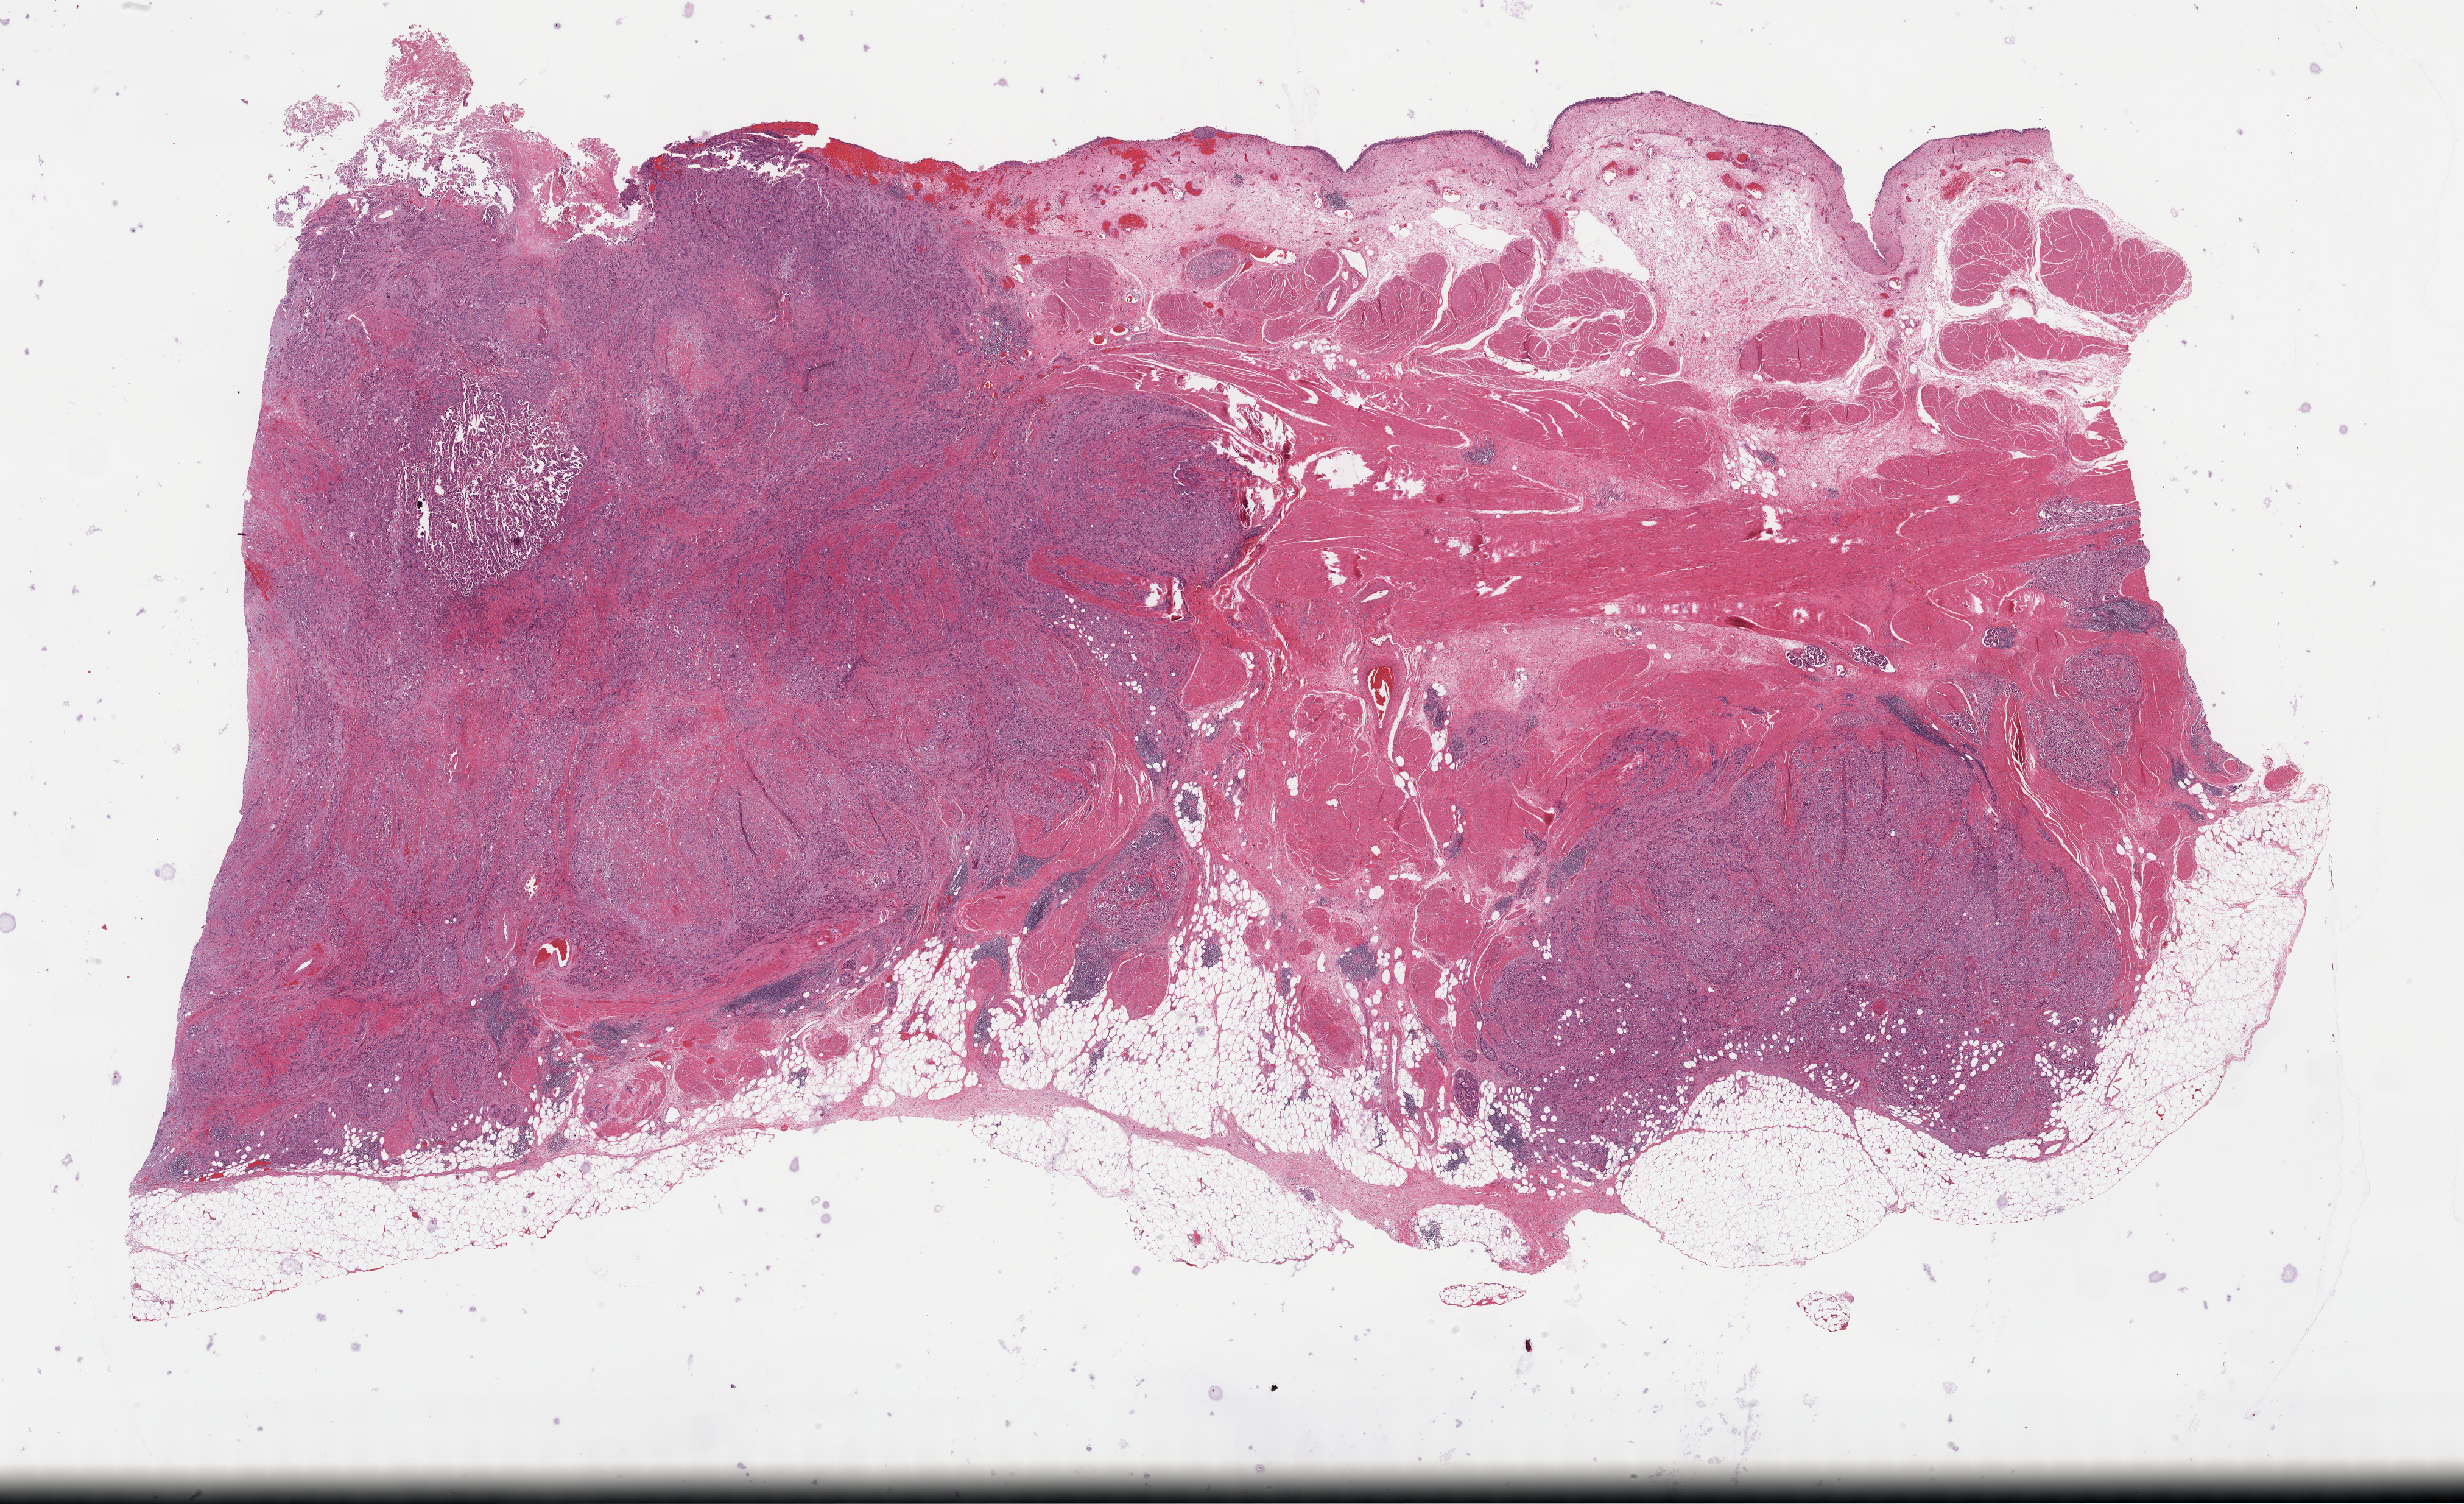
Hematoxylin and eosin (H&E) stained whole-slide image, whole scanned area (about 32.7 x 20.0 mm, acquisition: 40x scan) shown as a low-resolution overview. FFPE section. Sample: primary tumour, bladder. Male patient; age at initial diagnosis 63 years. Histologic grade: high grade.
* AJCC pathologic stage: IV
* lymph nodes positive (case pathology): 10 of 14 examined
* diagnosis: Transitional cell carcinoma (trigone of bladder)
* TNM: T3 N2 MX